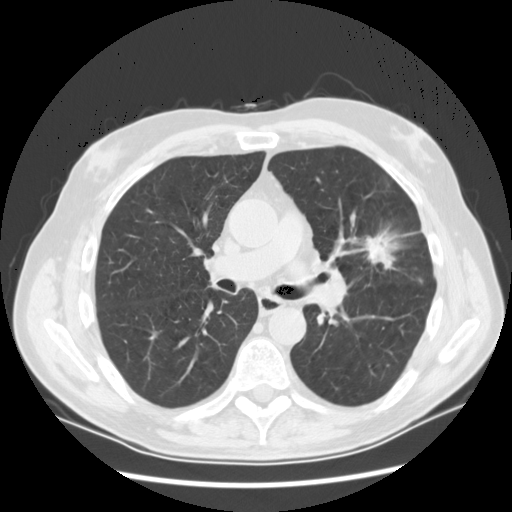
Low-dose screening chest CT, axial slice; baseline annual screen; lung window (W 1500 / L -600 HU); 2.5 mm slice thickness; standard (soft-tissue) reconstruction kernel (STANDARD); slice 56 of 132 in the series. Male, age 65 years at enrolment.
Expert-annotated lung lesion, box from (x=350, y=220) to (x=415, y=287) px. Screening reader's record for this exam (one nodule recorded; not confirmed to be the boxed lesion): non-calcified nodule or mass ≥4 mm, left upper lobe, 37 × 27 mm, spiculated (stellate) margins, soft tissue attenuation. Later outcome: lung cancer diagnosed 56 days after this screen — non-small cell carcinoma, poorly differentiated (G3), stage IA (AJCC 6th edition).